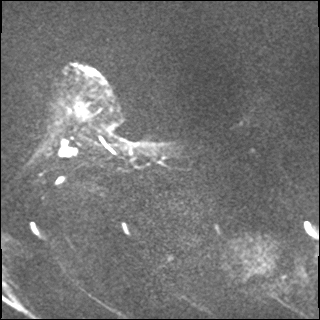
Breast MRI, one axial slice. Slice 7 of 37 in the series (ordered by position). Diffusion-weighted series; image 2 of 4 stored at this slice position (different b-values; order by instance number). 1.5 T. 4 mm slice thickness. 320 × 320 image matrix, field of view 320 × 320 mm. Female patient.
Annotated regions visible in this slice (manually delineated by an expert):
- tumour on diffusion-weighted imaging: bounding box (x1, y1, x2, y2) in pixels: (60, 138, 79, 156)